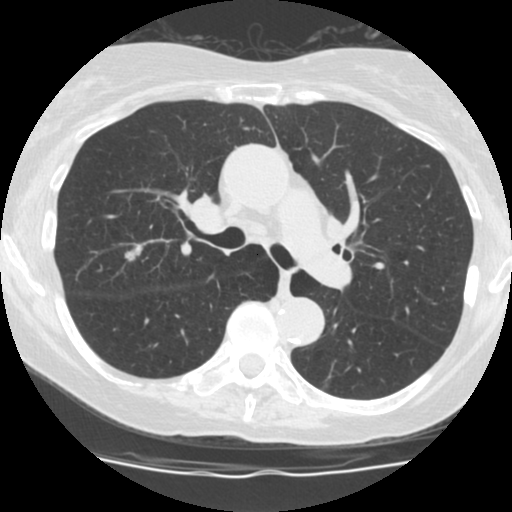
Low-dose screening chest CT, one axial slice; slice 116 of 183 in the series (ordered by position); reconstruction kernel STANDARD; lung window (W 1500 / L -600 HU); 2.5 mm slice thickness; 512 × 512 image matrix, field of view 300 × 300 mm.
Outlined on this slice (manually delineated by an expert):
- lesion 1 (tumor, upper lobe of right lung): box from (x=125, y=245) to (x=143, y=261) px